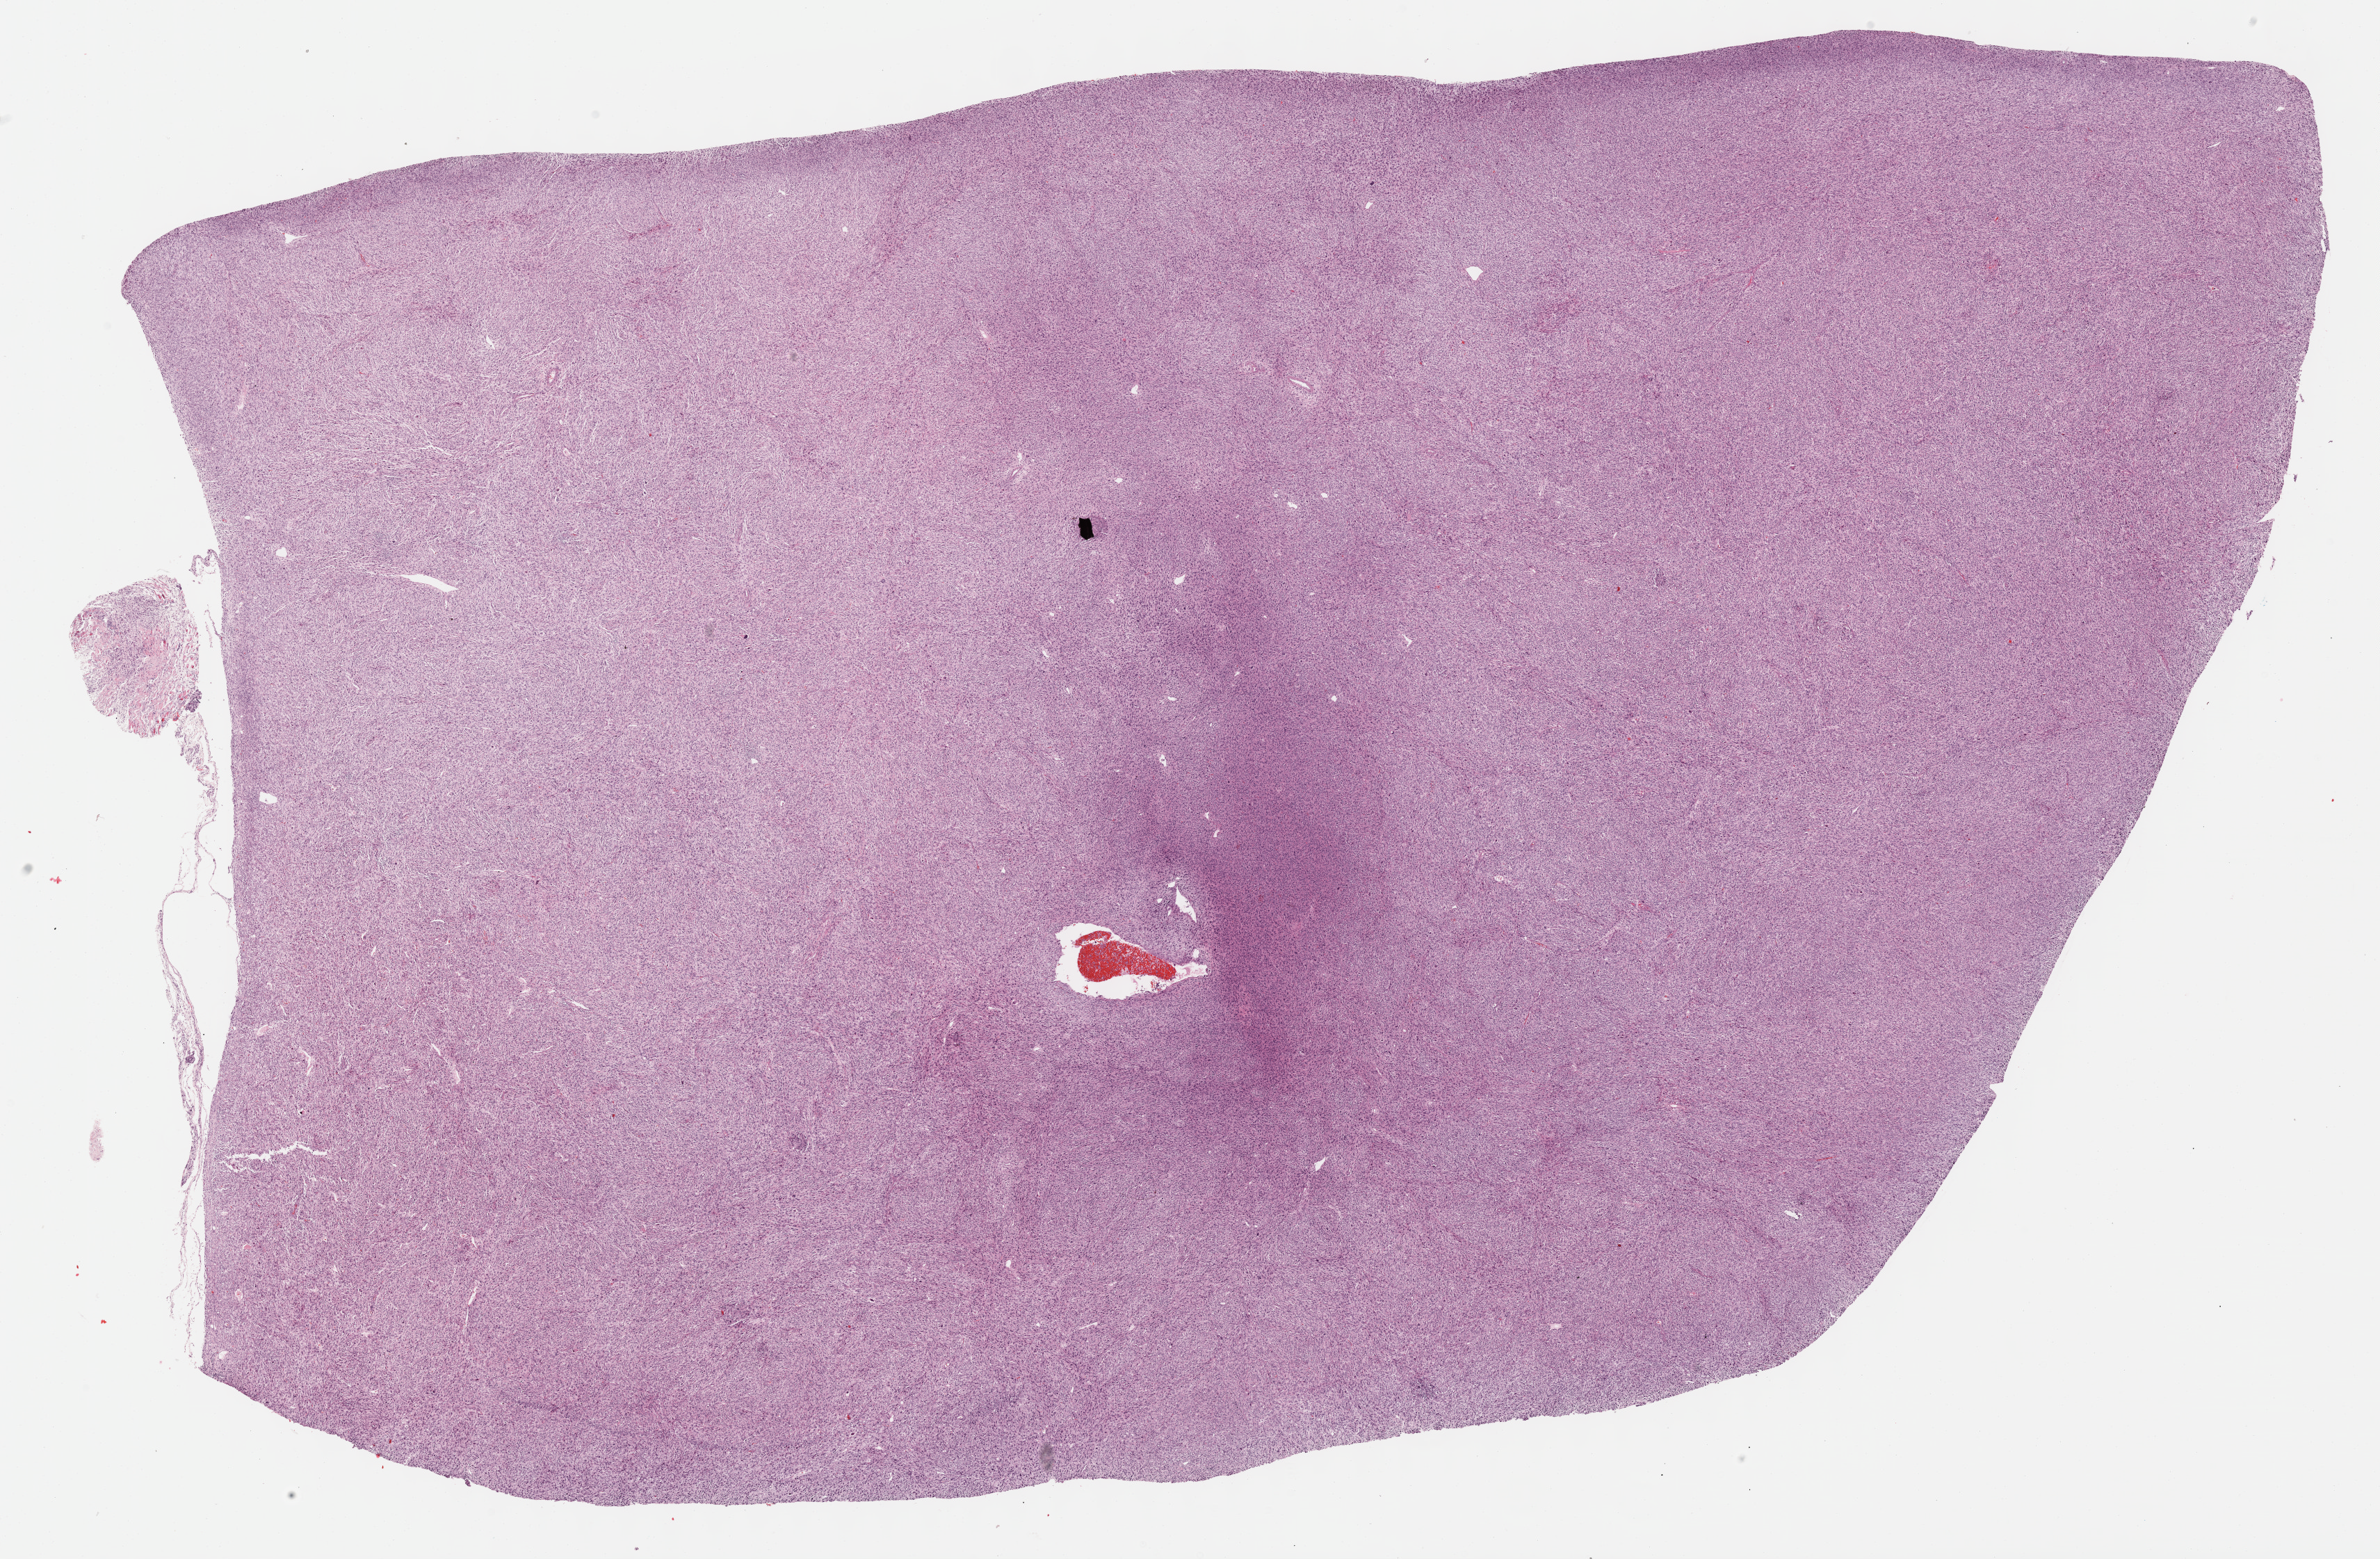
Whole-slide histology image, H&E-stained — low-resolution overview of the scanned area, about 27.7 x 18.1 mm. Formalin-fixed paraffin-embedded (FFPE) diagnostic section. Sample: primary tumour, connective, subcutaneous and other soft tissues. Female, age 61 years at initial diagnosis.
Pathologic diagnosis: Undifferentiated sarcoma (connective, subcutaneous and other soft tissues of lower limb and hip).